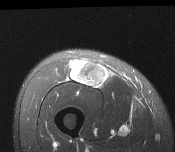
MRI of an extremity soft-tissue mass, one axial slice. Slice 56 of 116 in the series (ordered by position). T2-weighted fat-saturated. MR volume resampled by the dataset authors to the PET/CT grid (not the native acquisition matrix). 3.27 mm slice thickness. 175 × 152 image matrix. Male patient. From the clinical record (not read from this slice): histological type: pleiomorphic leiomyosarcoma; grade: intermediate; site of the primary tumour: right thigh.
Outlined on this slice (expert contour drawn on MRI and transferred to this co-registered scan by the dataset authors):
- gross tumour volume including surrounding oedema: box from (x=70, y=60) to (x=109, y=87) px